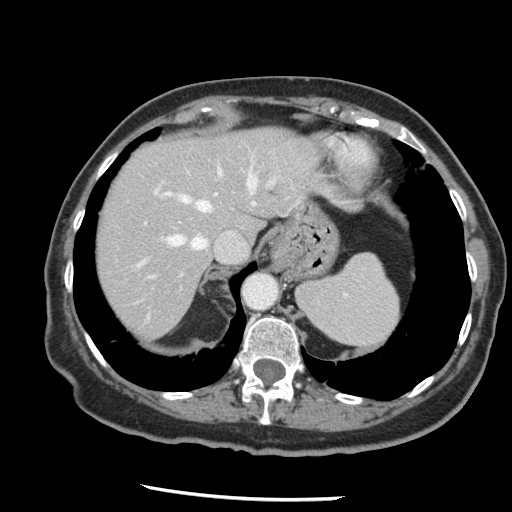
Contrast-enhanced abdominal CT, one axial slice. Position 107 of 148 along the scan axis. Reconstruction kernel STANDARD. 120 kVp. Intravenous contrast given. Soft-tissue window (W 400 / L 40 HU). 2.5 mm slice thickness. 512 × 512 image matrix, field of view 330 × 330 mm. Female patient, age 85 years. From the clinical record (not read from this slice): diagnosis: colorectal cancer liver metastases, imaged before liver resection; multiple liver metastases: no; largest metastasis: 0.9 cm.
Structures marked on this image (expert manual segmentation):
- hepatic veins: box from (x=139, y=152) to (x=279, y=265) px
- liver: (x=96, y=127)–(x=318, y=339)
- planned liver remnant (the part of the liver to remain after resection): (x=96, y=127)–(x=318, y=339)
- portal vein (with intrahepatic branches): (x=145, y=192)–(x=219, y=279)